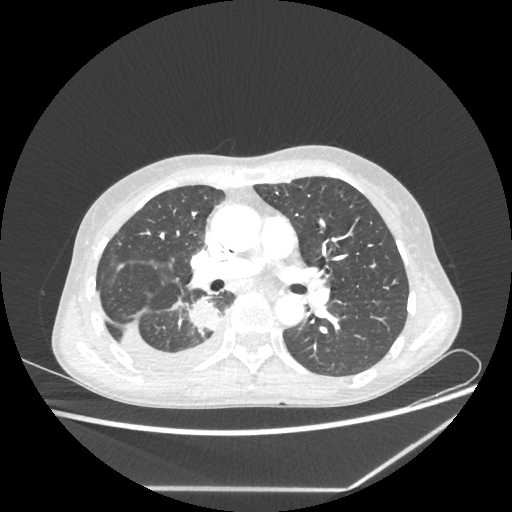
Chest CT, one axial slice. Position 132 of 237 along the scan axis. Reconstruction kernel STANDARD. 80 kVp. Lung window (W 1500 / L -600 HU). 512 × 512 image matrix. Patient: female, 59 years. From the clinical record (not read from this slice): clinical TNM (as recorded): T1c N1 M1.
Structures marked on this image (rectangle marked by the reading radiologist):
- lung tumour (recorded histology: adenocarcinoma): box from (x=187, y=298) to (x=221, y=334) px